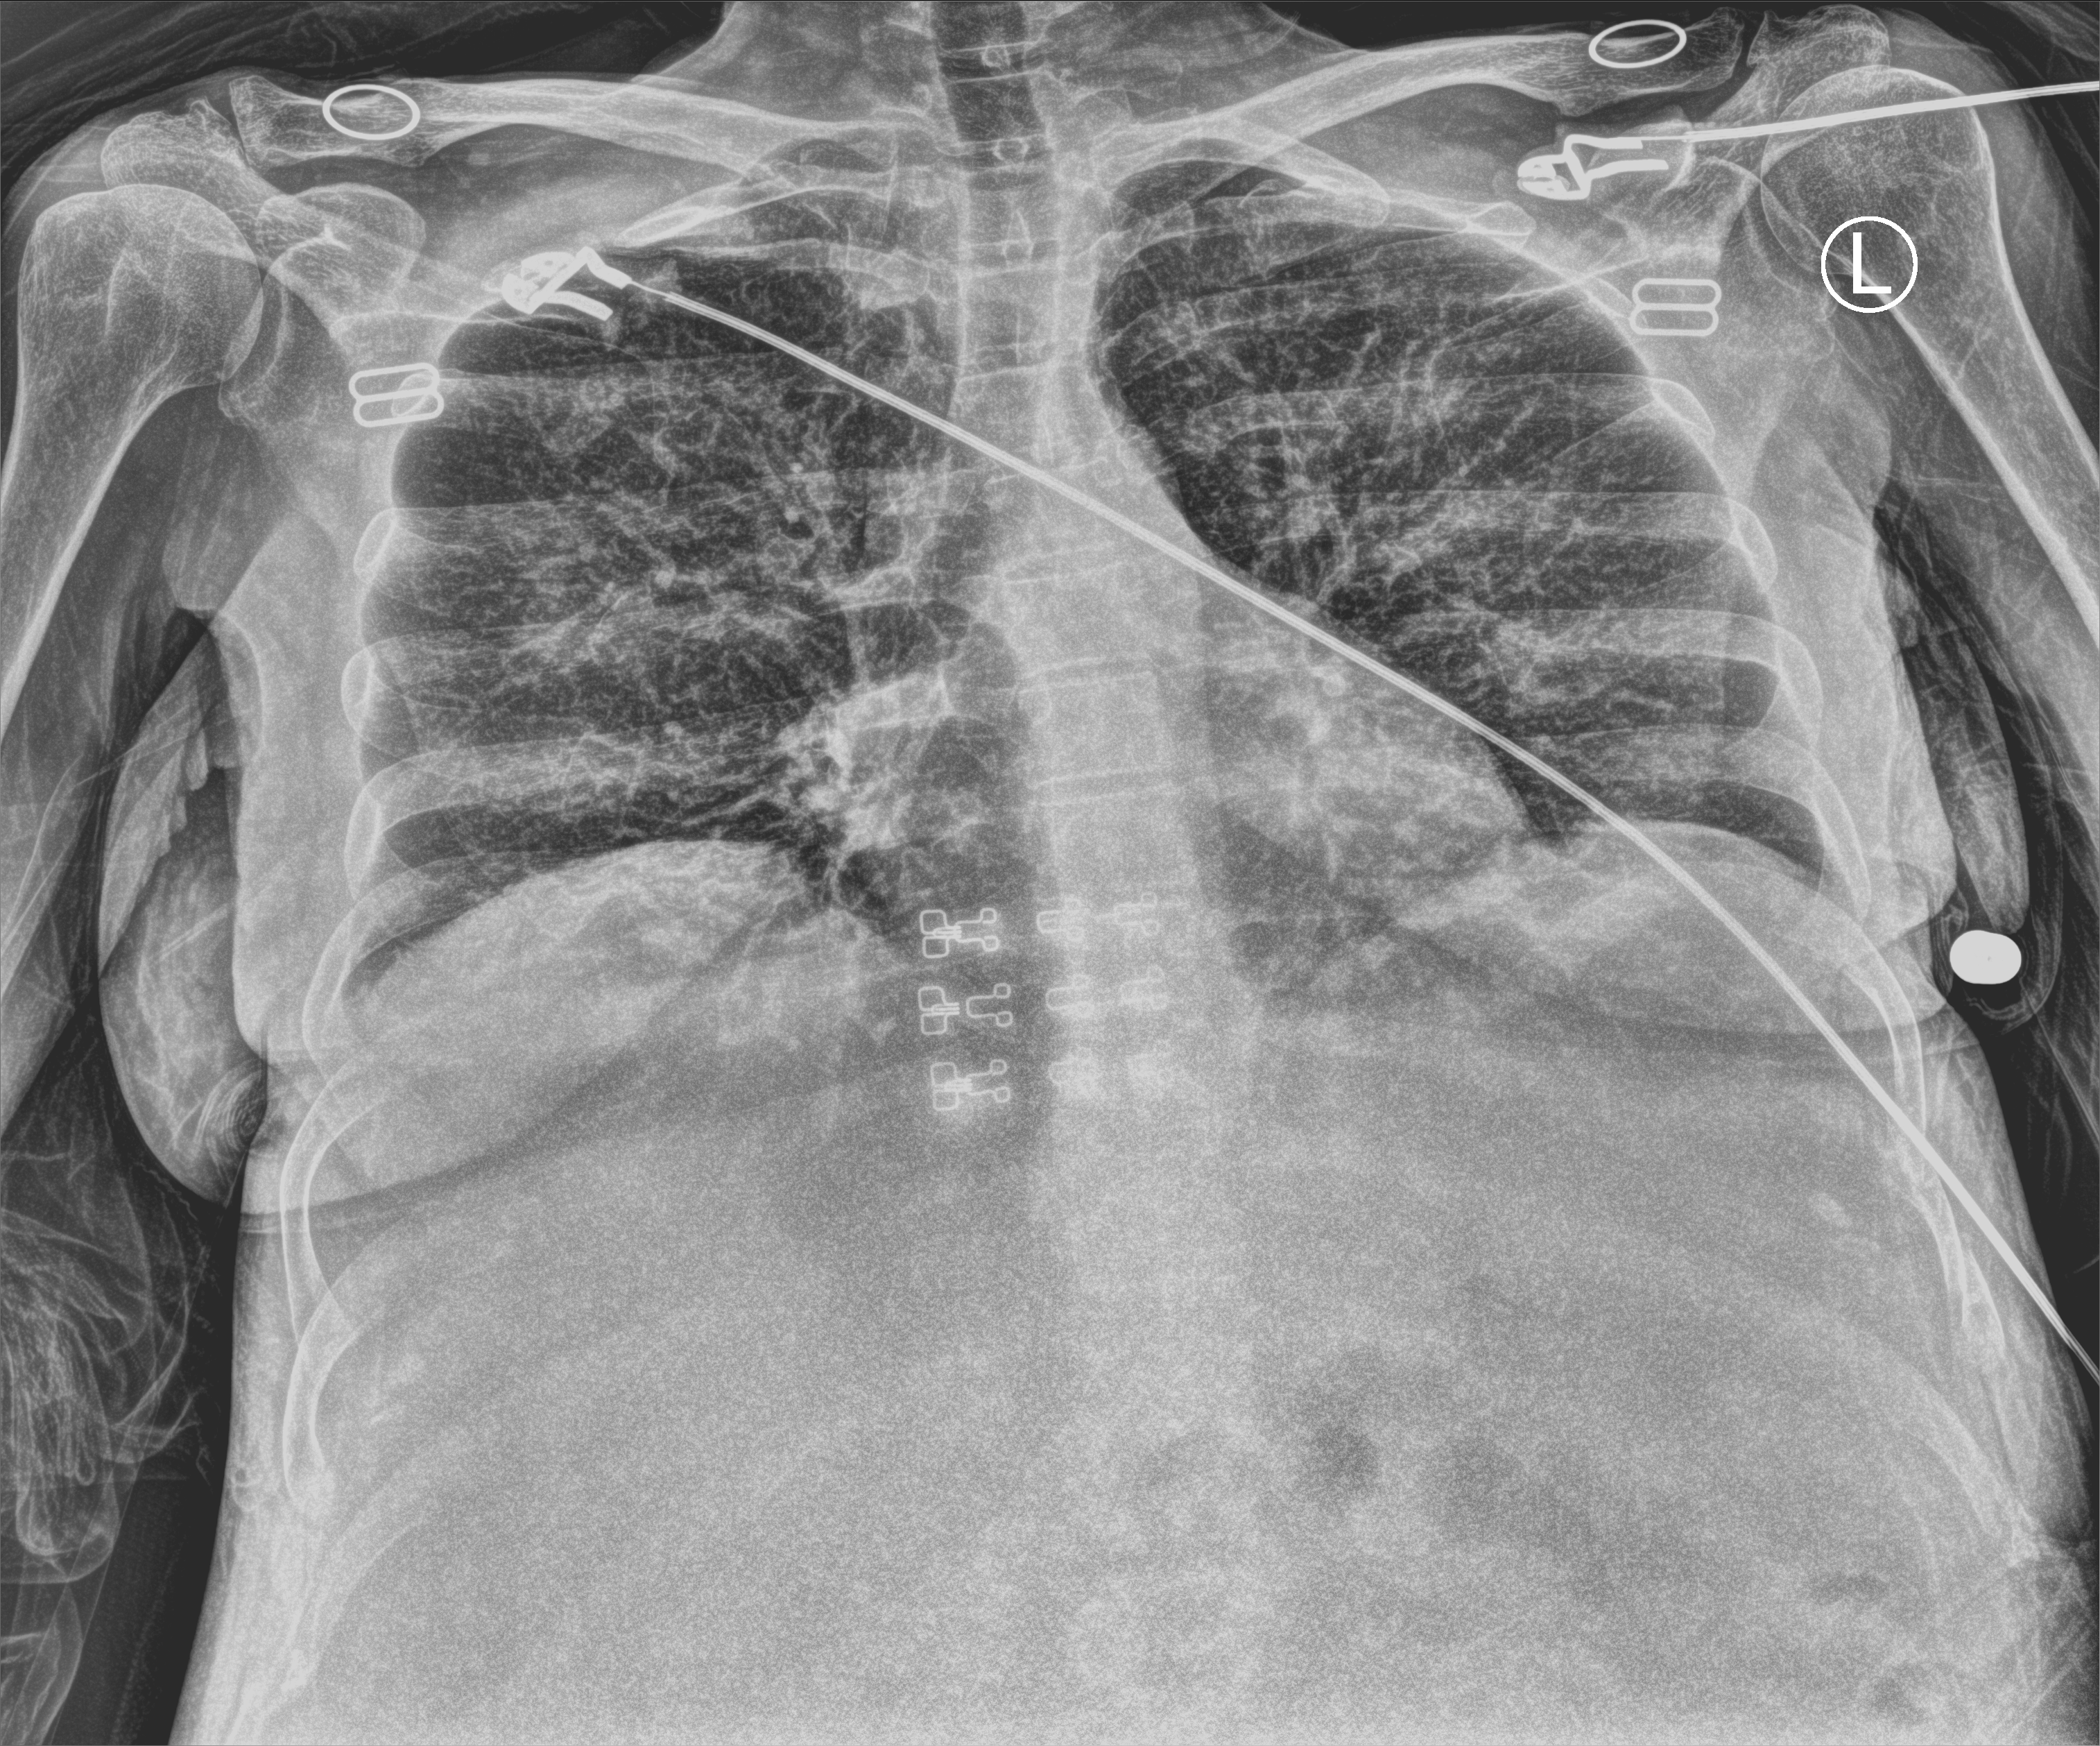
Bedside chest radiograph (computed radiography). Patient hospitalised with COVID-19; female, aged 18–59 years.
Hospital-stay facts (about this admission, not read from this image; timing relative to this image not recorded): COPD (admission record): no.